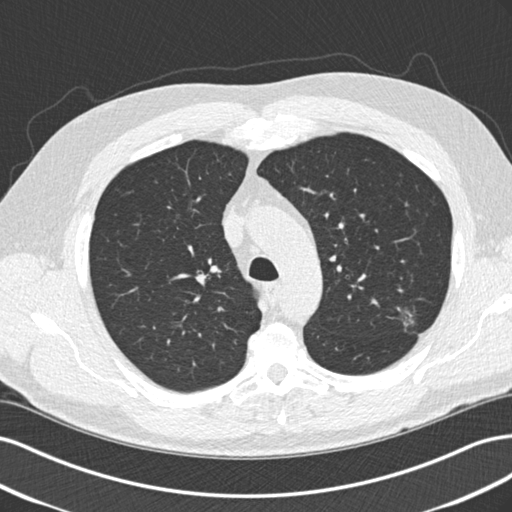
Low-dose screening chest CT, axial slice; second screening round (one year after baseline); lung window (W 1500 / L -600 HU); 120 kVp; slice 53 of 209 in the series. Male, age 65 years at enrolment.
Expert-annotated lung lesion, bounding box (x1, y1, x2, y2) in pixels: (388, 304, 425, 337). The exam's reader record, not a measurement of the box and not confirmed to be the same lesion: non-calcified nodule or mass ≥4 mm, left upper lobe, 10 × 9 mm, poorly defined margins, mixed attenuation, pre-existing on the prior screen: yes; interval growth: no. Lung cancer was diagnosed 221 days after this screen: adenocarcinoma, NOS, left upper lobe, poorly differentiated (G3), stage IA (AJCC 6th edition), 13 mm at pathology.